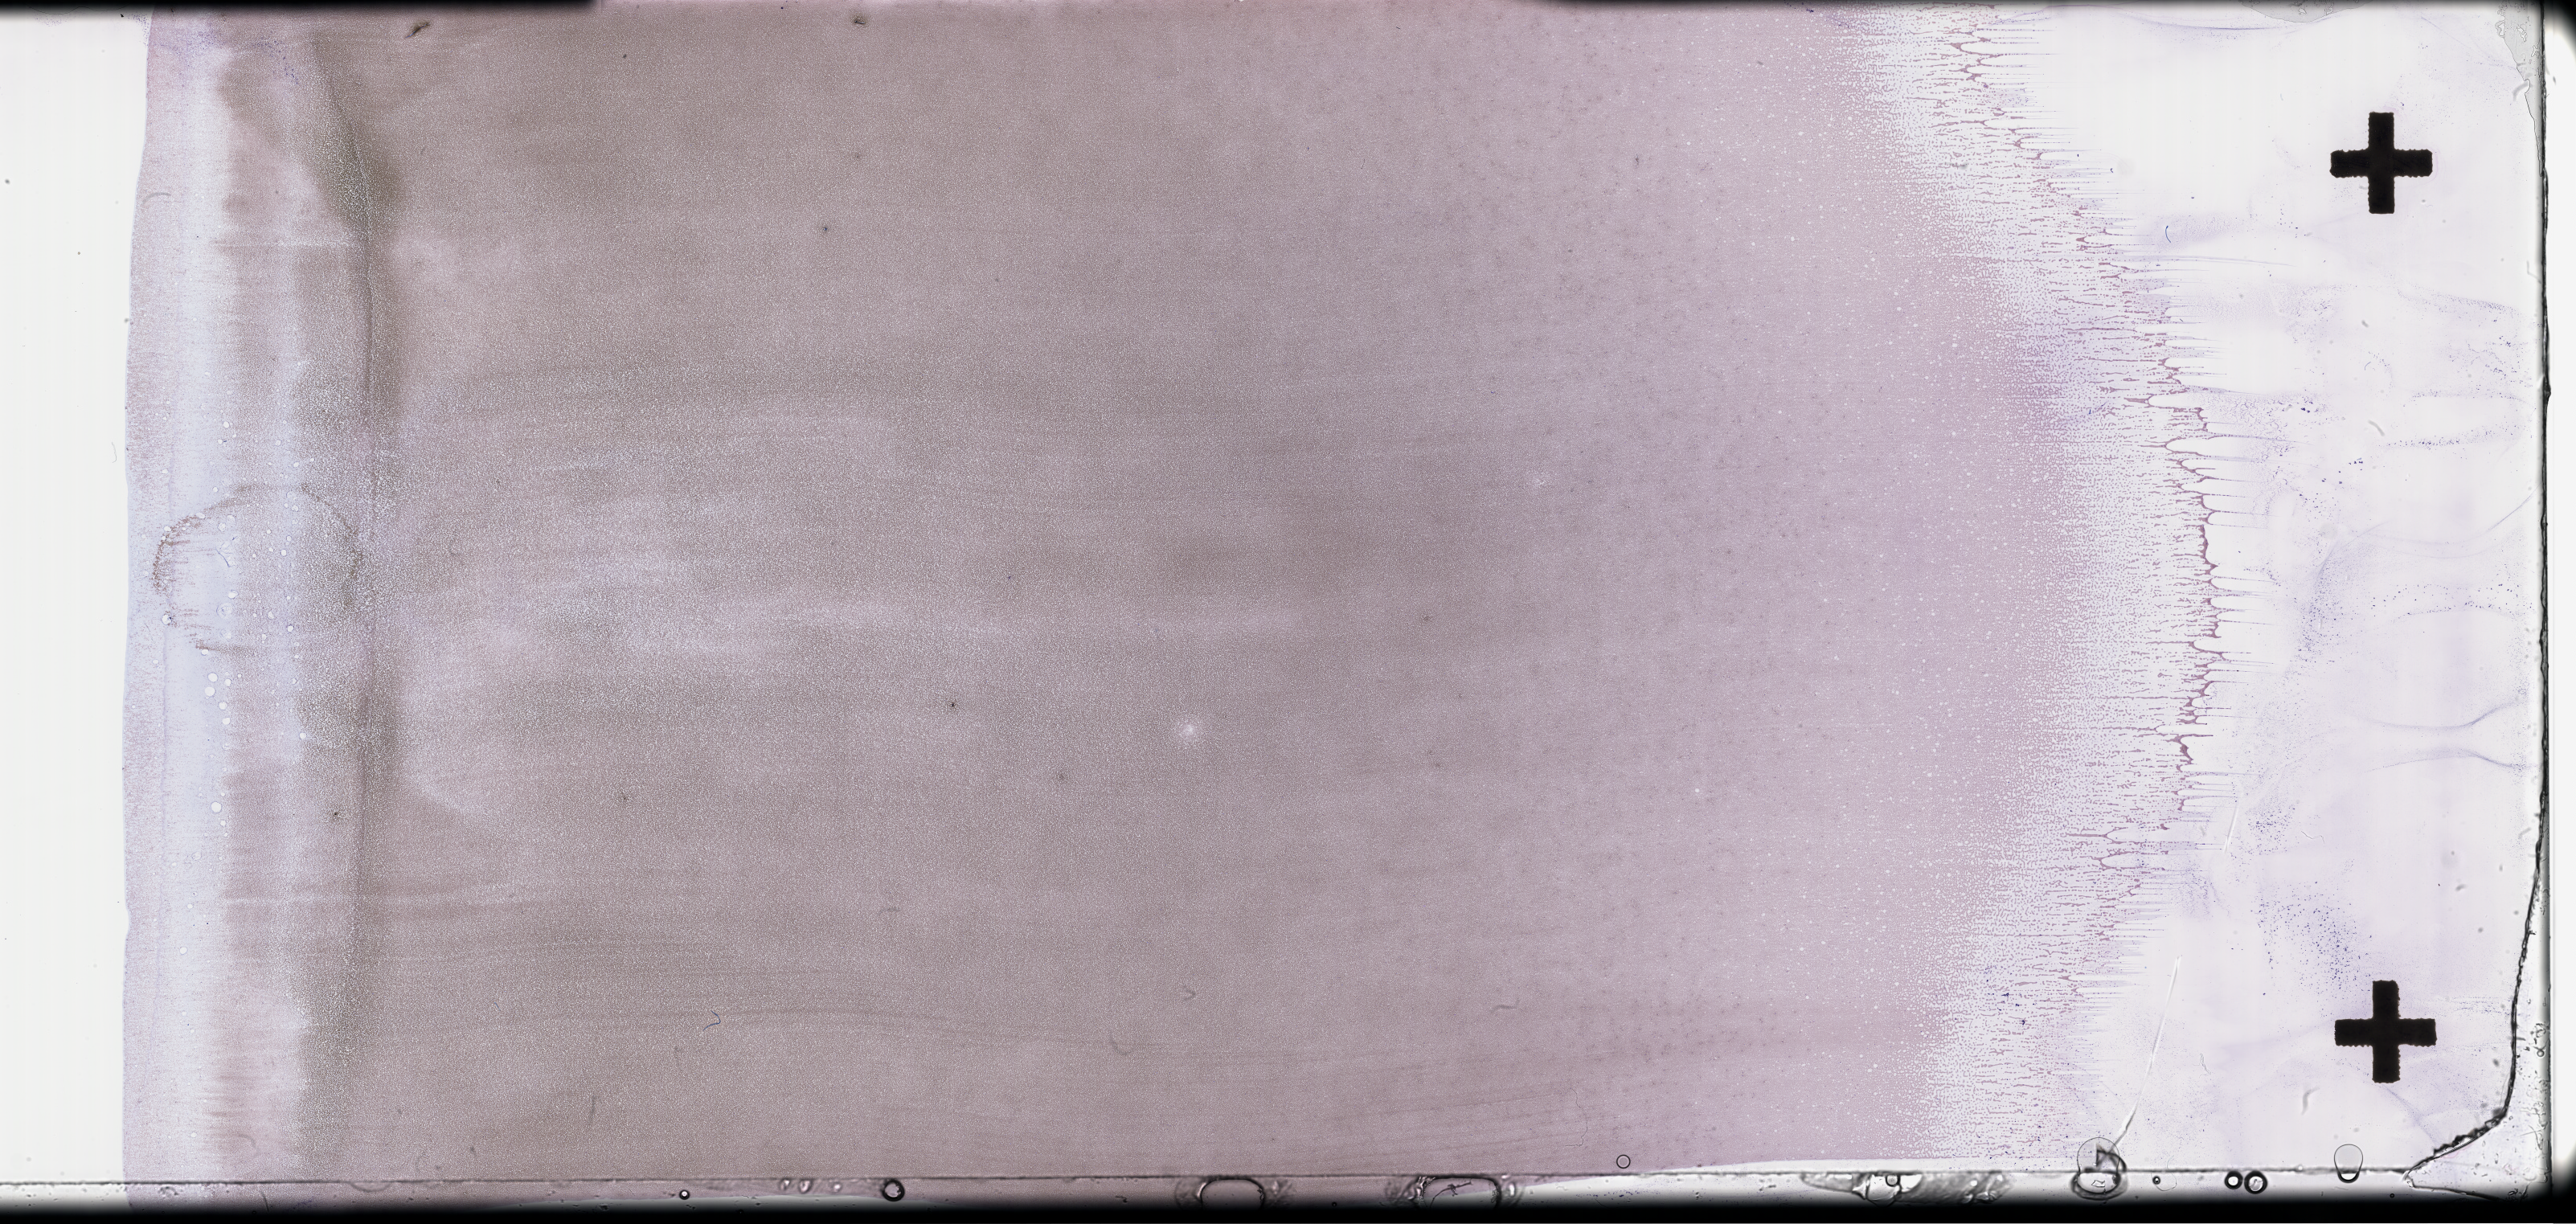
Whole-slide image of a whole blood smear, Wright-Giemsa stain — whole scanned area (about 51.8 x 24.6 mm) shown as a low-resolution overview, collected on treatment. Patient: male.
- patient diagnosis: Plasma Cell Myeloma